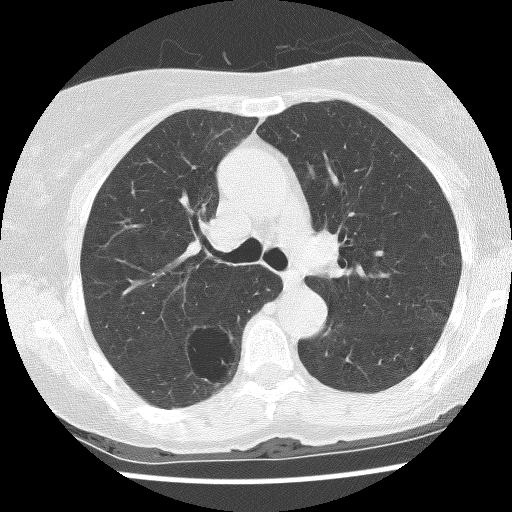
Low-dose screening chest CT, axial slice, first (baseline) screen, lung window (W 1500 / L -600 HU), lung (sharp) reconstruction kernel (BONE), slice 44 of 136 in the series, 512 × 512 image matrix, field of view 300 × 300 mm. Female, age 69 years at enrolment. Former smoker at enrolment.
Lesion marked by an expert reader, bounding box (x1, y1, x2, y2) in pixels: (168, 323, 244, 397). The screening reader recorded 2 non-calcified nodules or masses ≥4 mm on this exam (right lower lobe, right lower lobe); which of them this box marks is not recorded. Later outcome: lung cancer diagnosed 288 days after this screen — non-small cell carcinoma, right lower lobe, poorly differentiated (G3), stage IB (AJCC 6th edition), 36 mm at pathology.